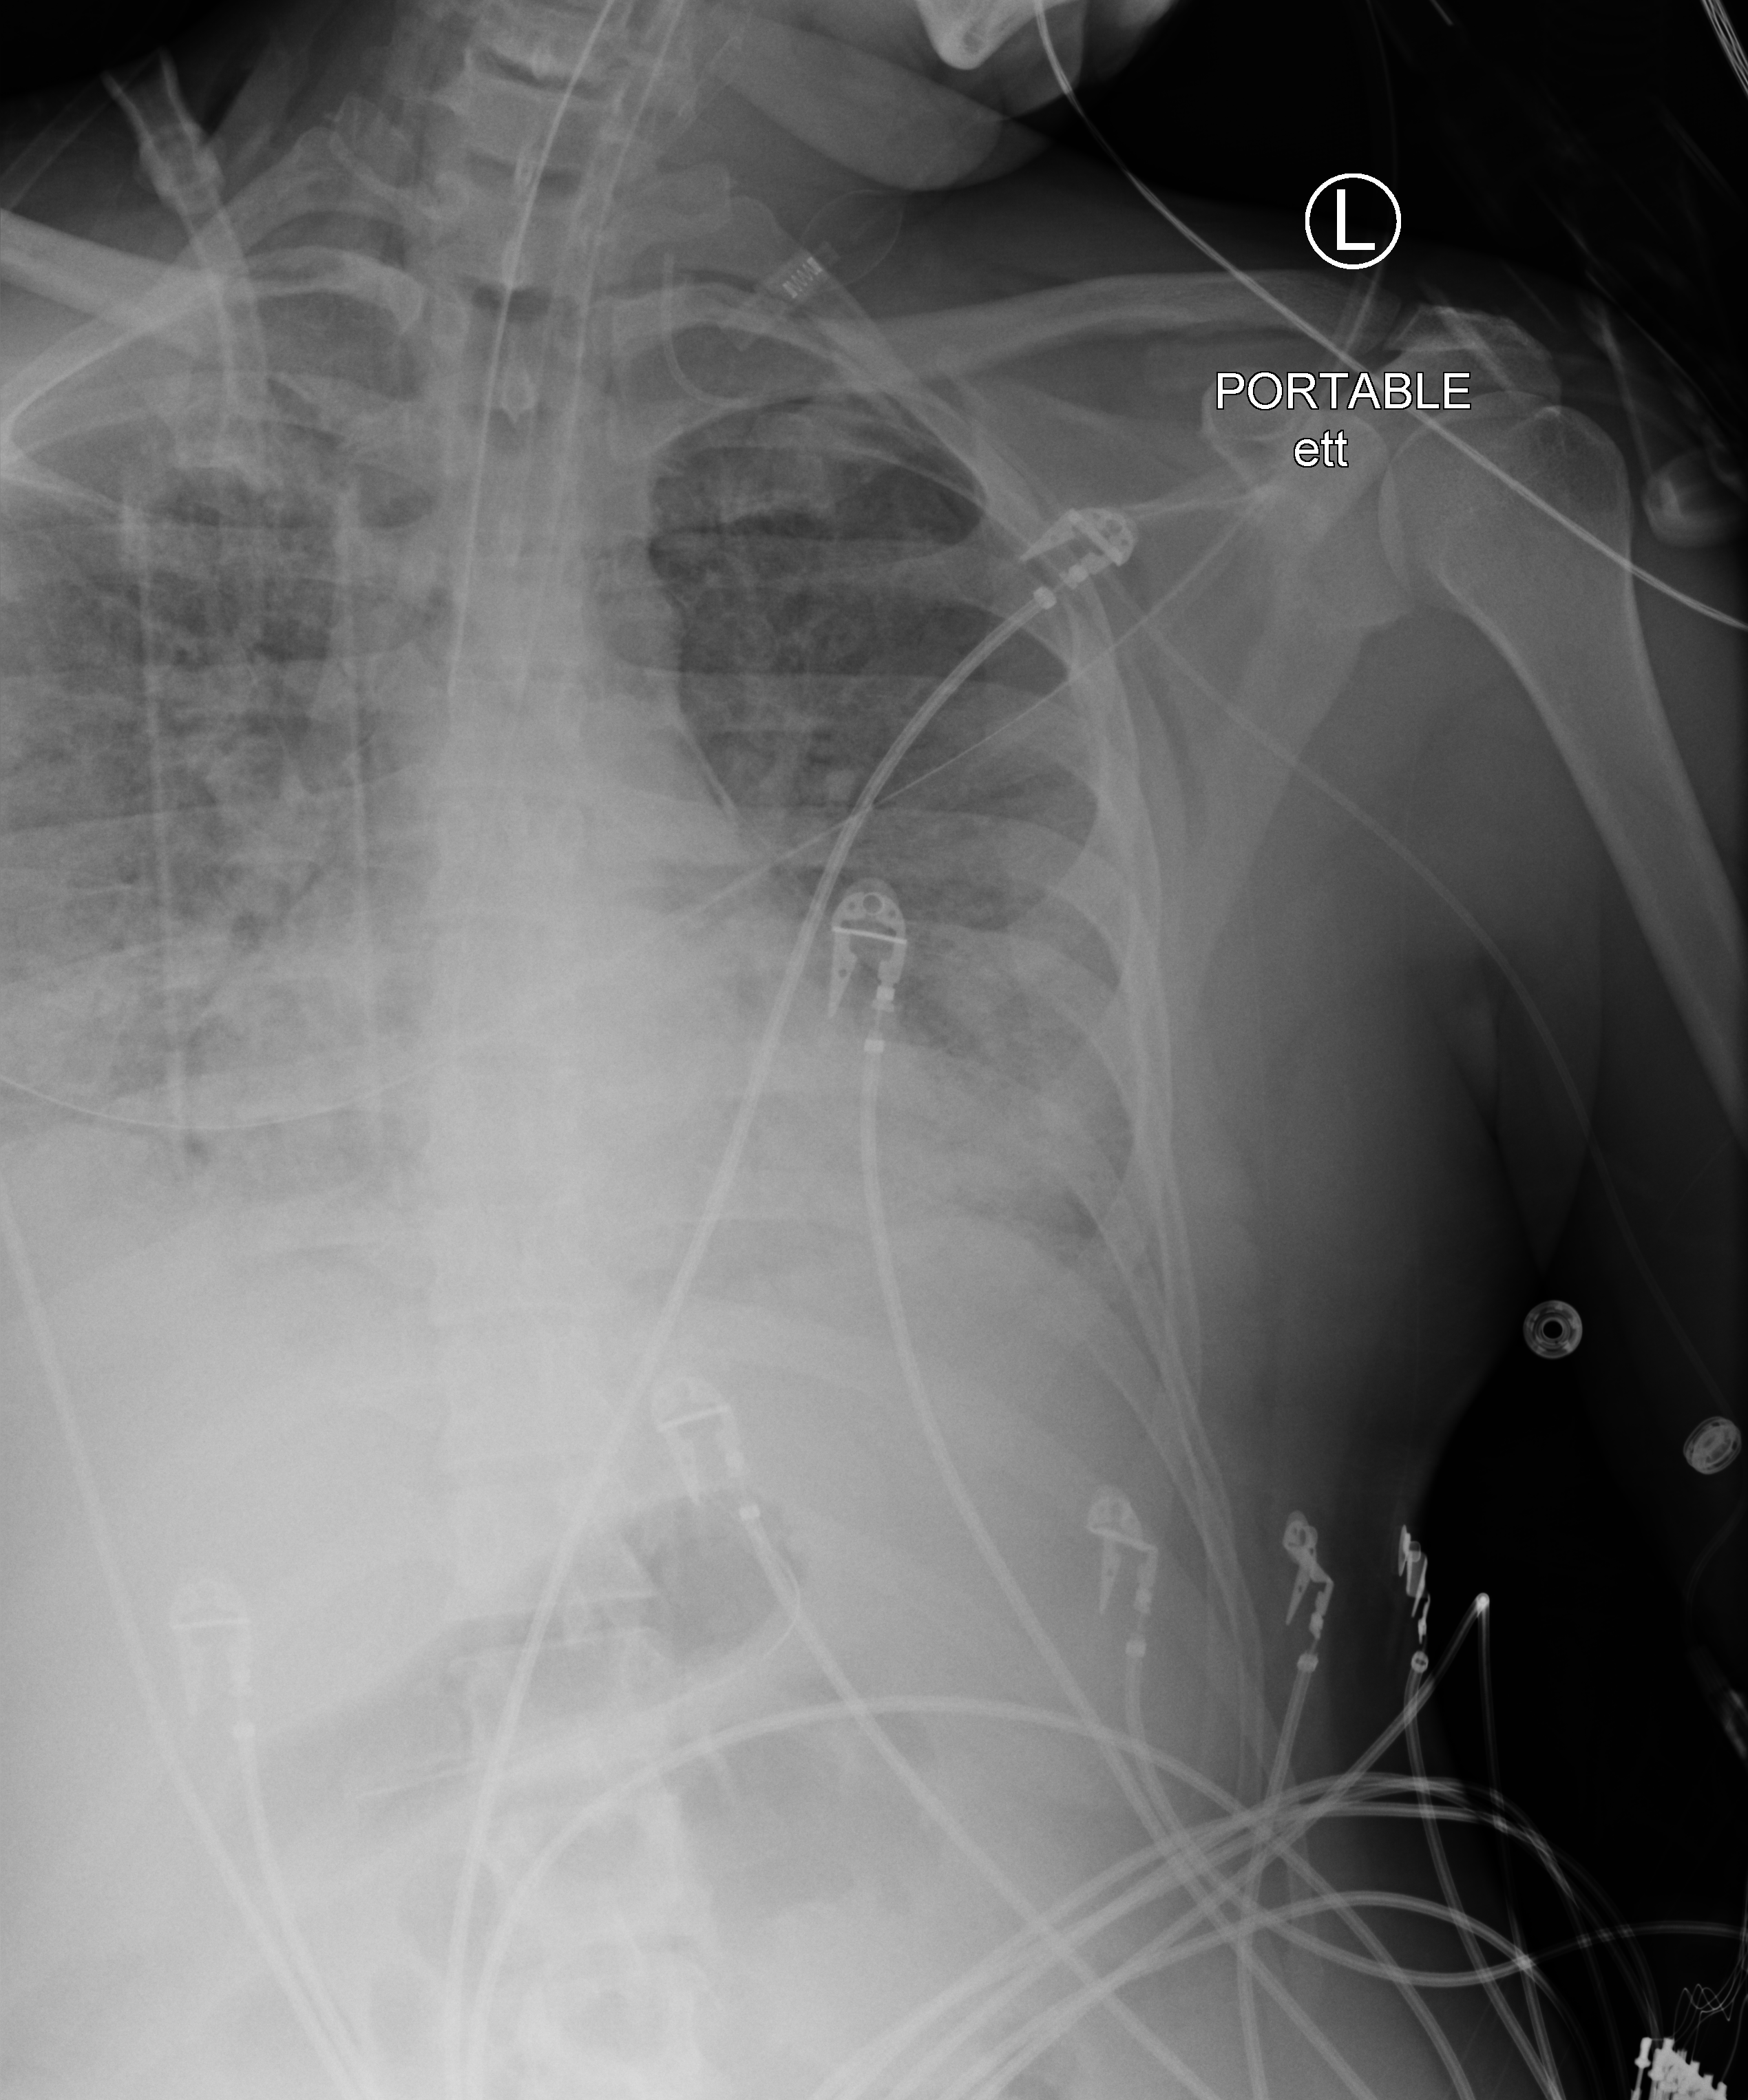
Bedside chest radiograph (computed radiography); anteroposterior (AP) projection. Male patient hospitalised with COVID-19, age 18–59 years.
Hospital-stay facts (about this admission, not read from this image; timing relative to this image not recorded):
- diabetes (admission record): no